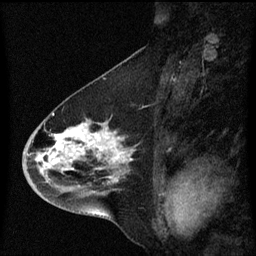
Breast MRI (dynamic contrast-enhanced), one sagittal slice; position 30 of 60 along the scan axis; dynamic contrast-enhanced series, image 2 of 3 at this slice position (ordered by acquisition); 1.5 T; TE 4.2 ms, TR 8.4 ms; 256 × 256 image matrix, field of view 200 × 200 mm. Patient: female, 46 years. From the clinical record (not read from this slice): setting: breast cancer imaged before/during neoadjuvant chemotherapy; receptor status: HER2-positive.
Annotated regions visible in this slice (semi-automatic segmentation, software-assisted and operator-edited):
- analysis volume of interest (the breast-tissue region the enhancement analysis was run in; not a lesion): bounding box [x1, y1, x2, y2] px = [23, 112, 137, 195]
- tumour enhancement mask (voxels above the 70 % enhancement threshold inside the analysis volume of interest): [40, 128, 130, 183]